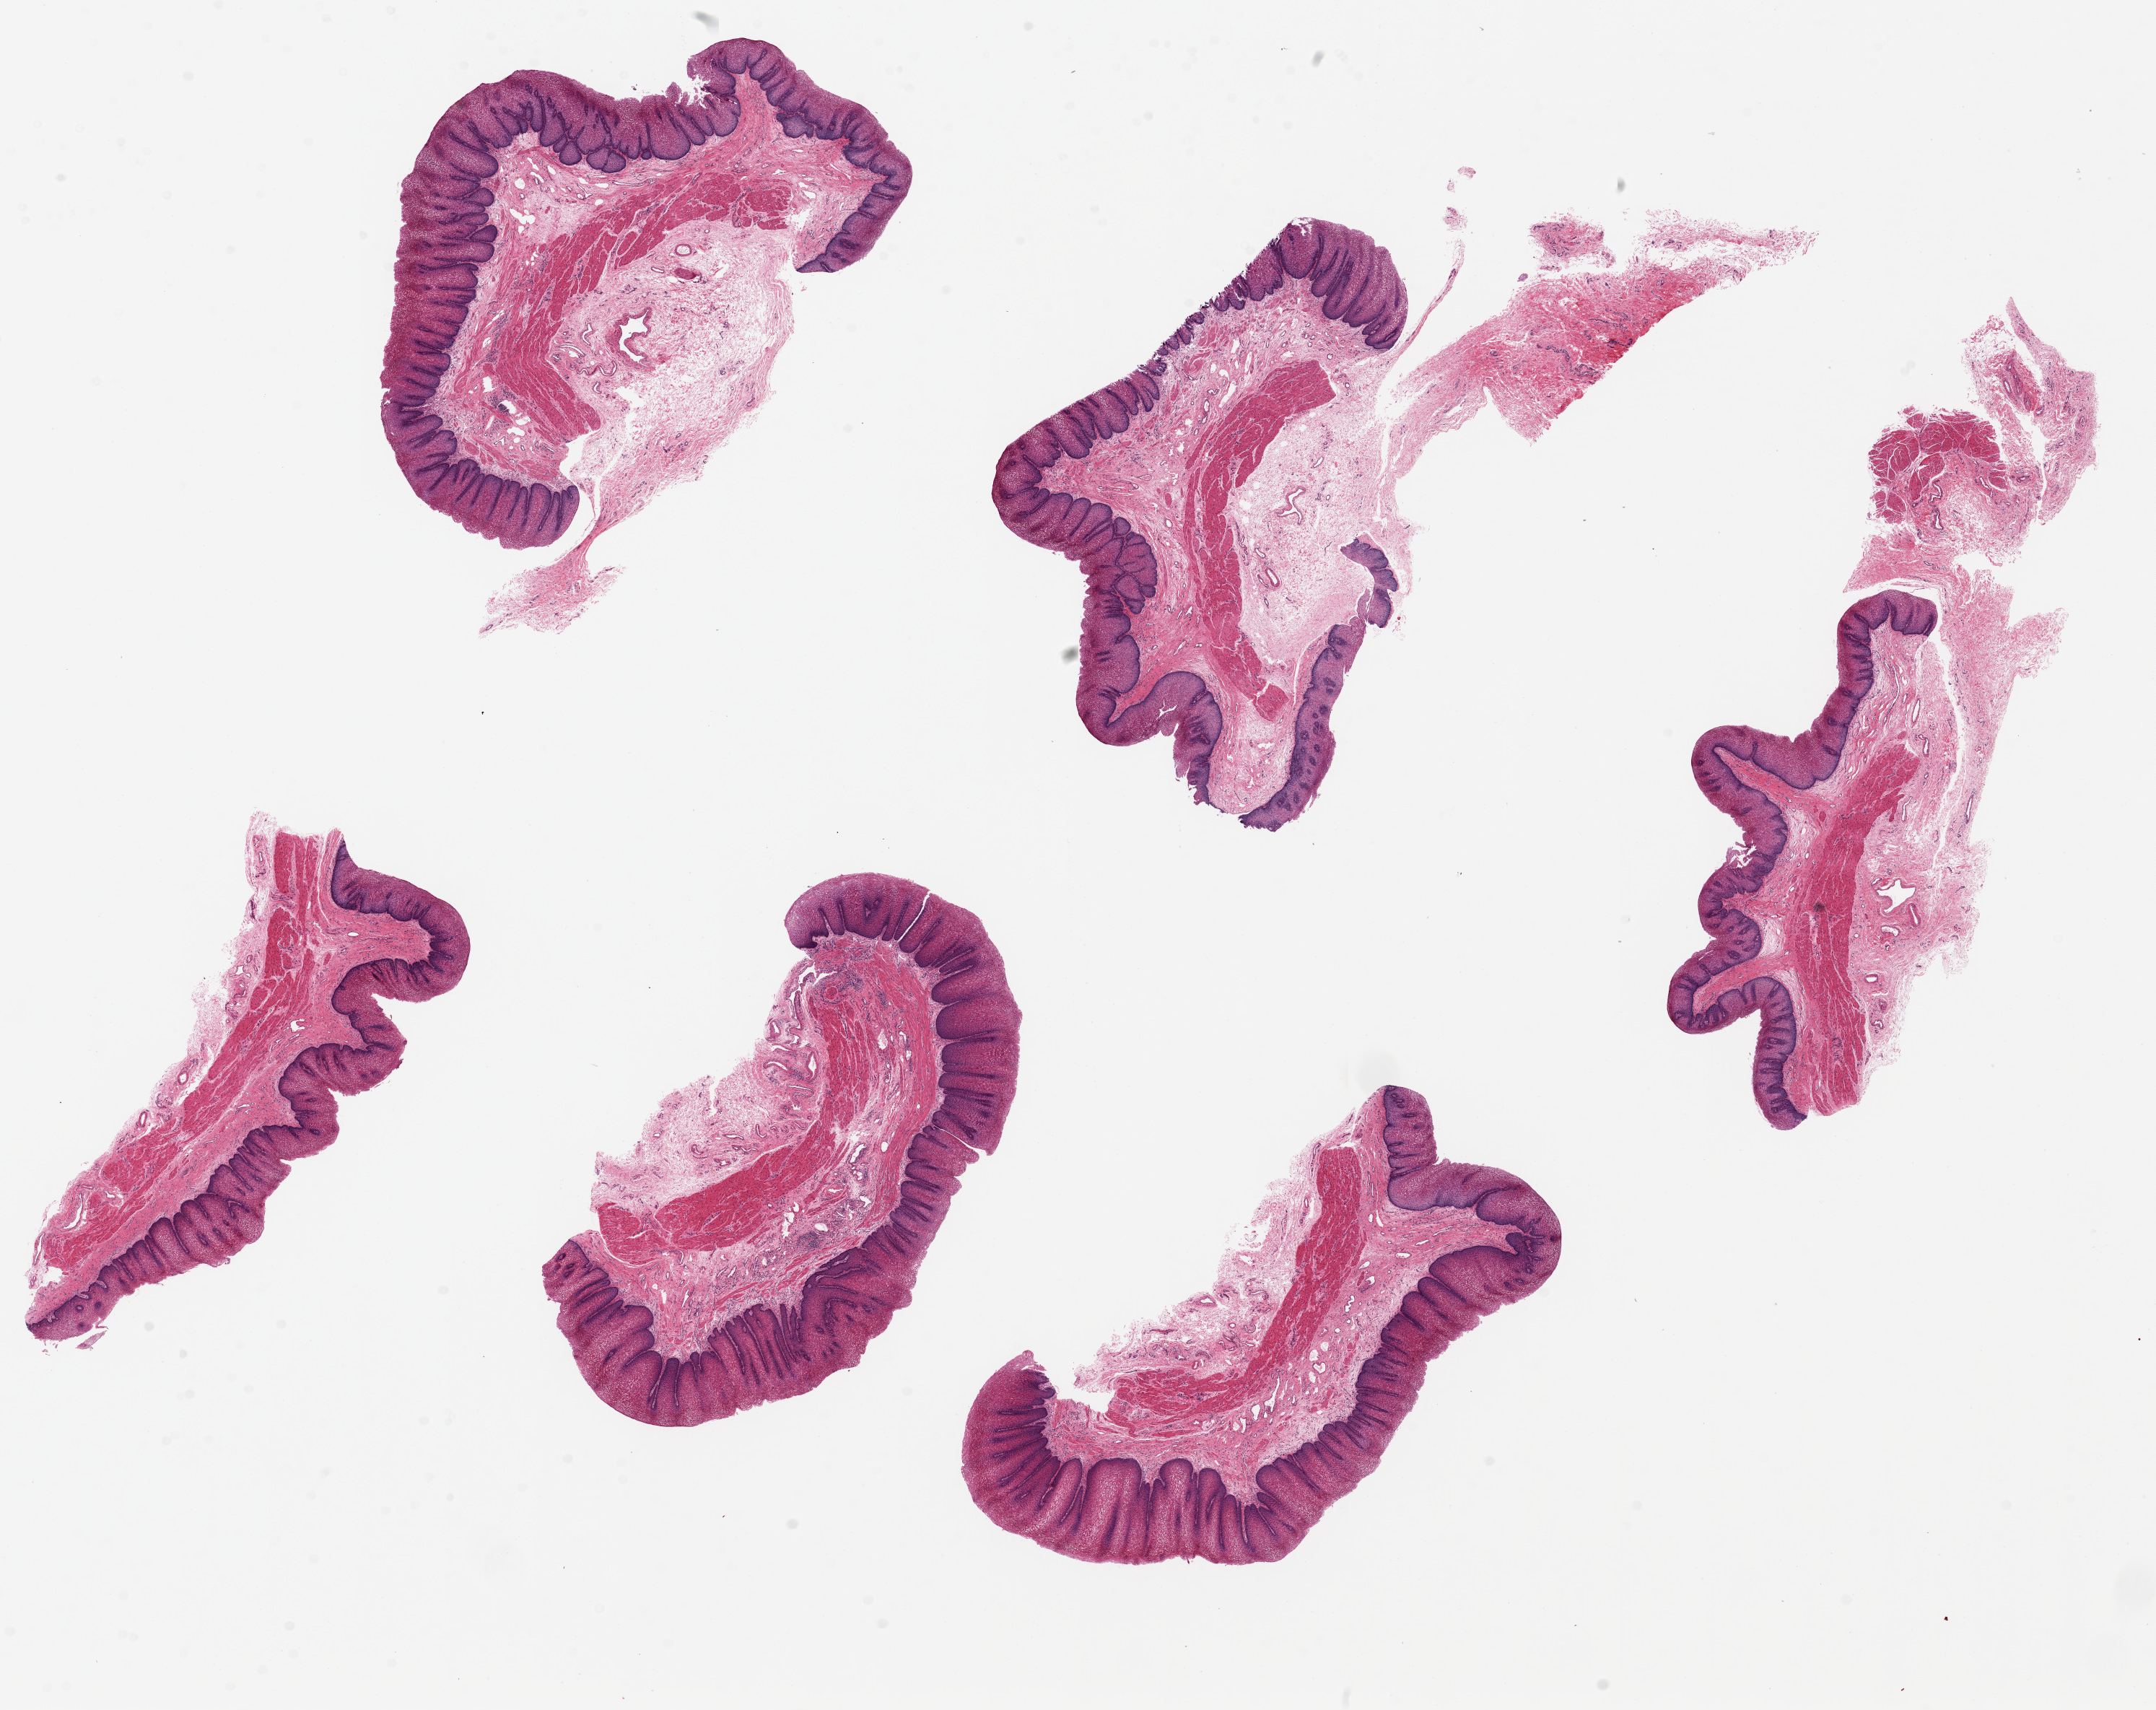
H&E whole-slide image, a low-resolution overview of the entire scanned area, about 23.6 x 18.7 mm. PAXgene-fixed, paraffin-embedded tissue. Target tissue: esophageal mucous membrane. Donor tissue sample.
Reviewer comment on this tissue sample: 6 pieces, up to 9.5x3mm; hyperplastic squamous epithelium.